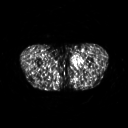
FDG PET of an extremity soft-tissue mass (from a PET/CT study), one axial slice. Slice 253 of 311 in the series (ordered by position). 128 × 128 image matrix, field of view 500 × 500 mm. Patient: male, 29 years. Case-level facts recorded for this patient, not image findings: histological type: mixoid liposarcoma; grade: low; site of the primary tumour: left thigh.
Structures marked on this image (expert contour drawn on MRI and transferred to this co-registered scan by the dataset authors):
- gross tumour volume (mass): bounding box (x1, y1, x2, y2) in pixels: (71, 54, 82, 66)